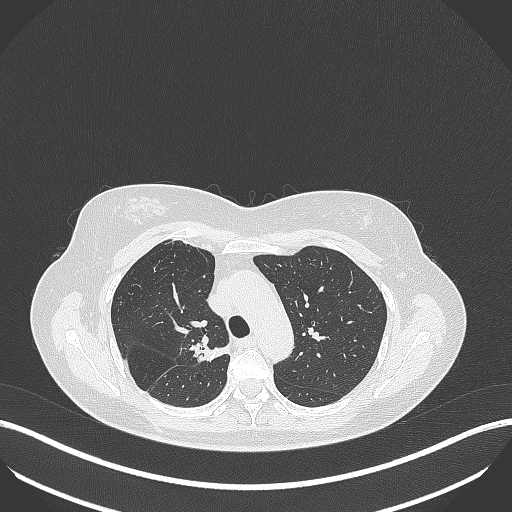
Chest CT, one axial slice; slice 281 of 386 in the series (ordered by position); reconstruction kernel B70f; 120 kVp; lung window (W 1500 / L -600 HU); 1 mm slice thickness; 512 × 512 image matrix, field of view 400 × 400 mm. Patient: female, 65 years. From the clinical record (not read from this slice): clinical TNM (as recorded): T1b N0 M0; histopathological grade: G2.
Annotated regions visible in this slice (rectangle marked by the reading radiologist):
- lung tumour (recorded histology: adenocarcinoma): bounding box (x1, y1, x2, y2) in pixels: (189, 337, 233, 364)